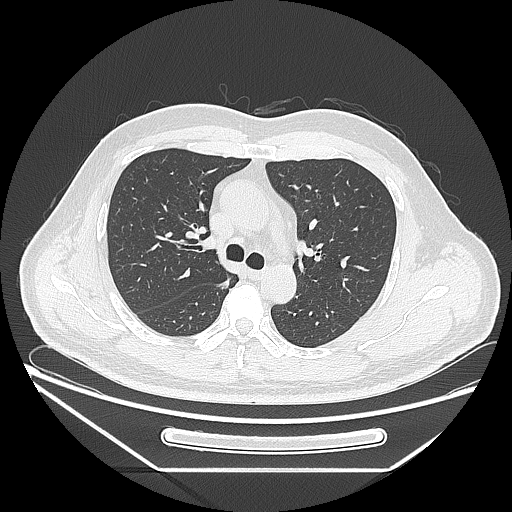
Chest CT, one axial slice. Slice 168 of 271 in the series (ordered by position). Reconstruction kernel LUNG. 120 kVp. Lung window (W 1500 / L -600 HU). 512 × 512 image matrix. Patient: male, 49 years. Case-level facts recorded for this patient, not image findings: clinical TNM (as recorded): T1b N0 M0; histopathological grade: G2.
Annotated regions visible in this slice (rectangle marked by the reading radiologist):
- lung tumour (recorded histology: adenocarcinoma): bounding box [x1, y1, x2, y2] px = [212, 276, 236, 293]